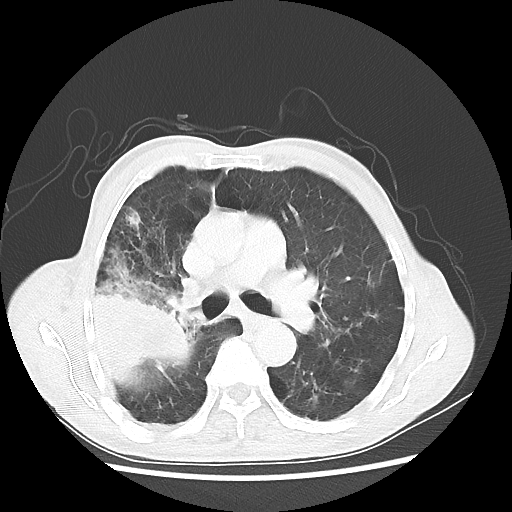
Chest CT, one axial slice; reconstruction kernel LUNG; 100 kVp; lung window (W 1500 / L -600 HU); 5 mm slice thickness; 512 × 512 image matrix, field of view 351 × 351 mm. Male patient, age 75 years. From the clinical record (not read from this slice): clinical TNM (as recorded): T4 N1 M1.
Outlined on this slice (bounding box drawn by a radiologist):
- lung tumour (recorded histology: adenocarcinoma): bounding box [x1, y1, x2, y2] px = [83, 270, 202, 389]